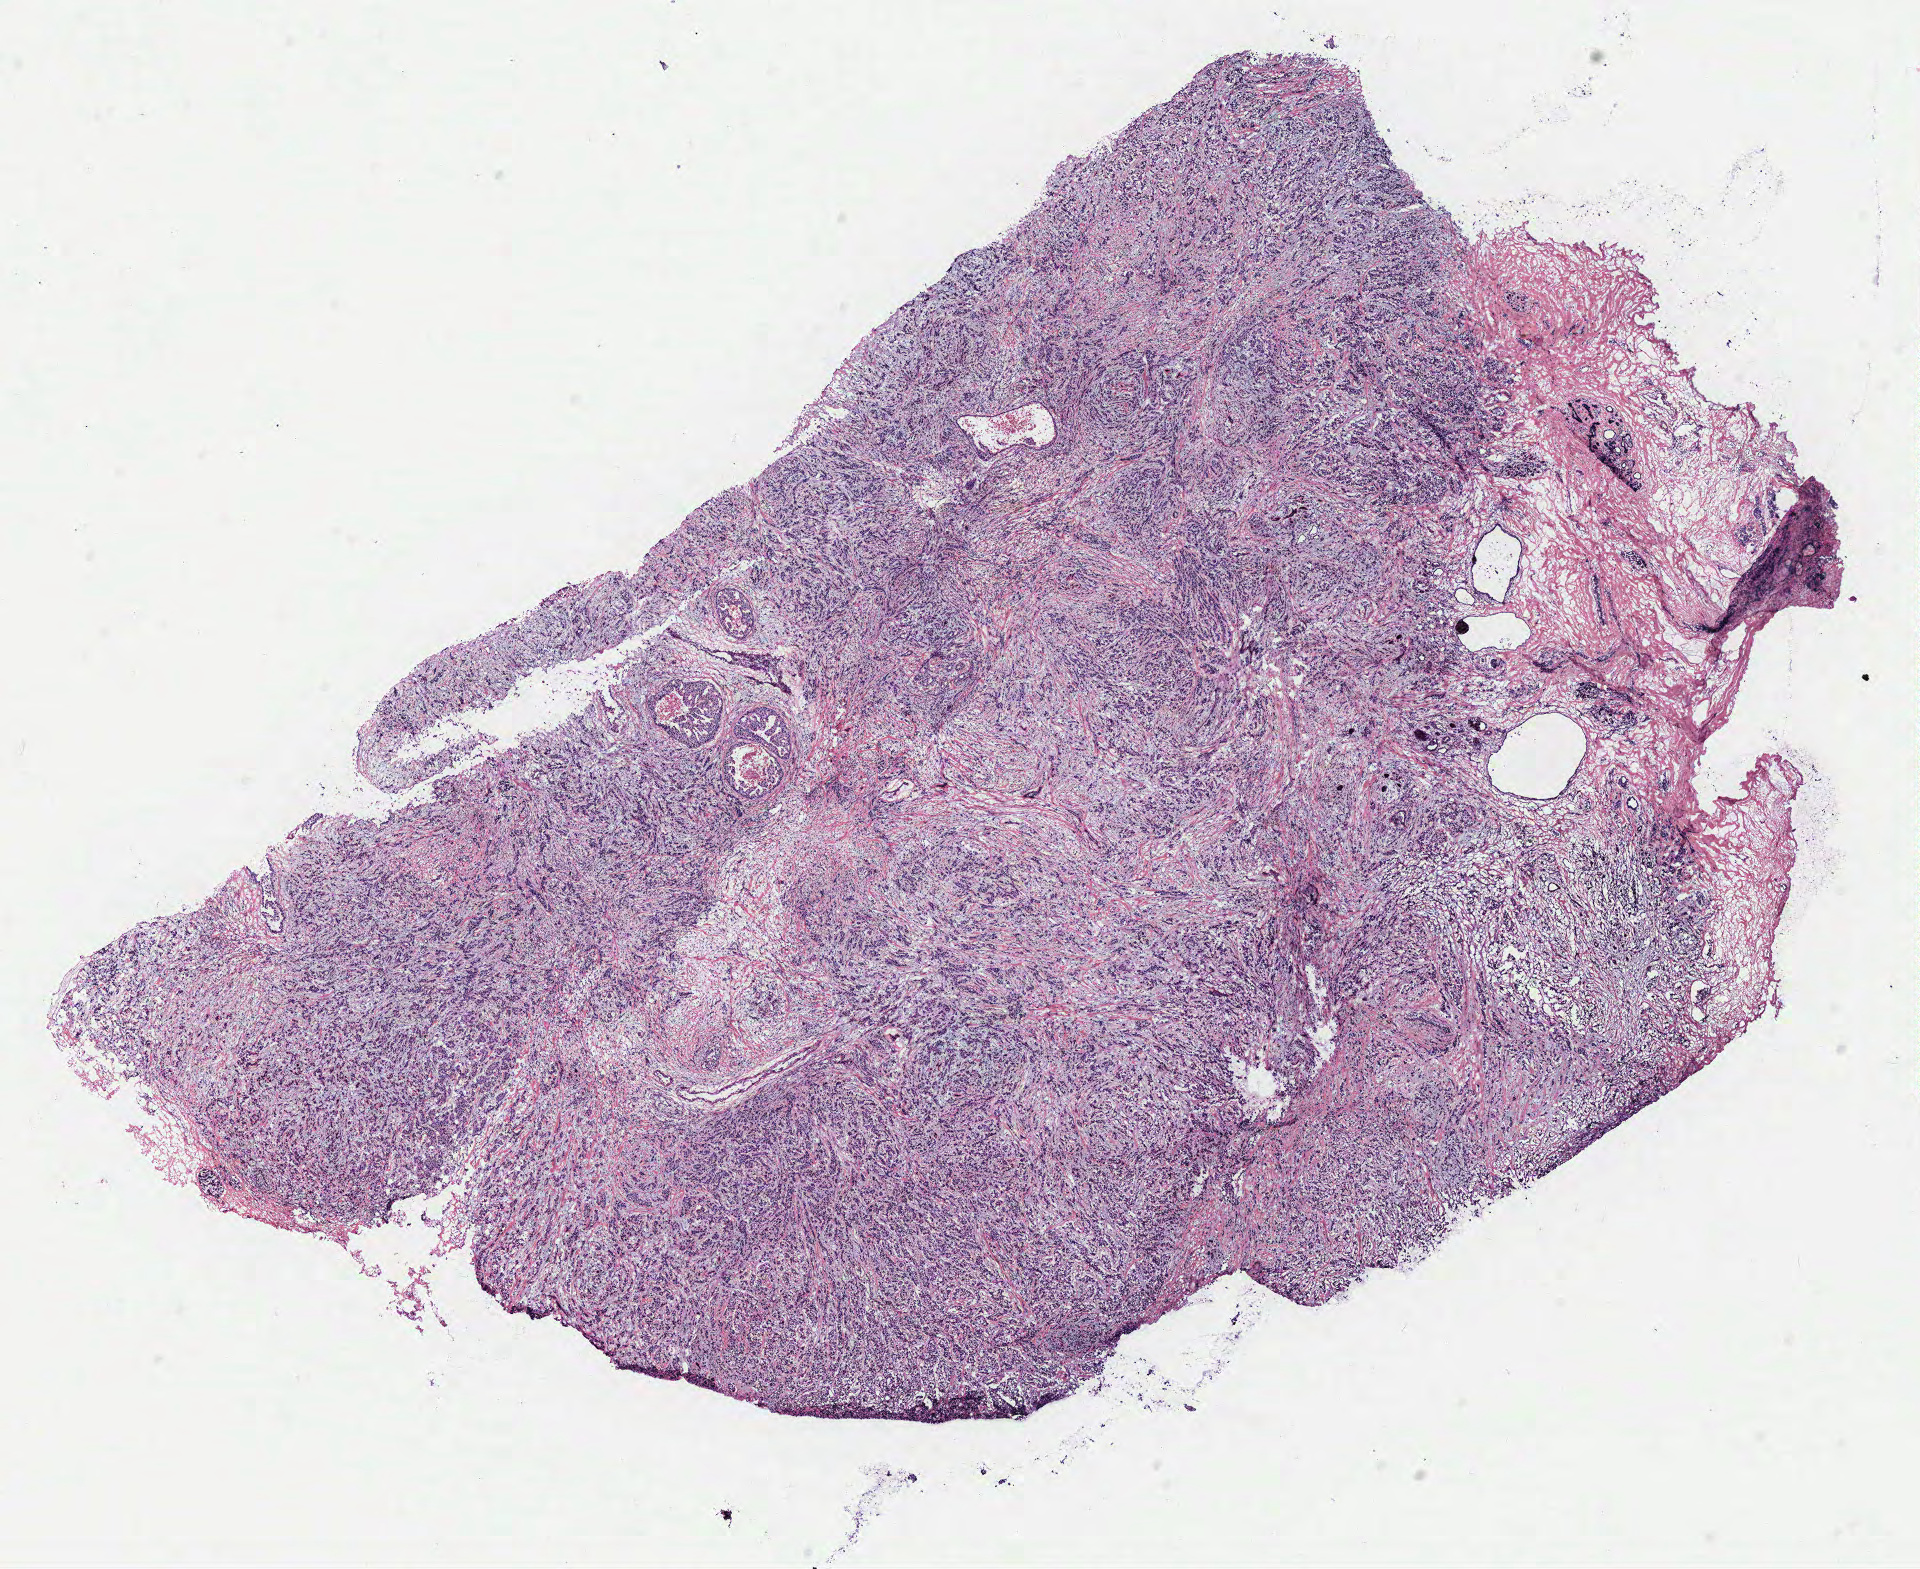
Whole-slide histology image, H&E, whole scanned area (about 15.4 x 12.6 mm) shown as a low-resolution overview. Breast, tissue type not recorded. Patient: female, age 48 years.
Patient diagnosis: Infiltrating duct carcinoma, NOS.